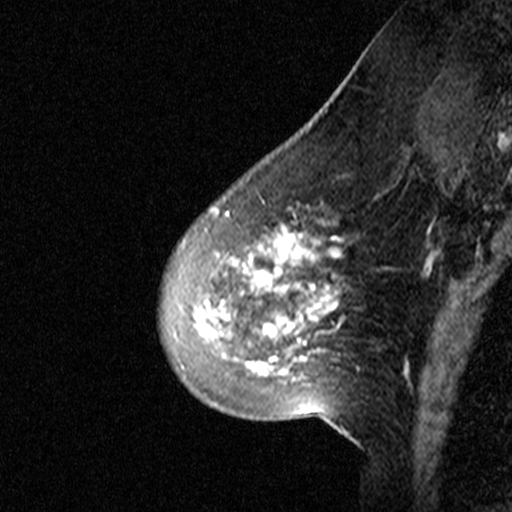
Breast MRI (dynamic contrast-enhanced), one sagittal slice. Slice 12 of 44 in the series (ordered by position). Dynamic contrast-enhanced study with each time point stored as its own series, time point 2 of 3 at this slice position (early post-contrast, ordered by acquisition time). 1.5 T. TE 4.5 ms, TR 11 ms. 3 mm slice thickness. 512 × 512 image matrix, field of view 200 × 200 mm. Patient: female, 46 years. Case-level facts recorded for this patient, not image findings: setting: breast cancer imaged before/during neoadjuvant chemotherapy; receptor status: HER2-positive.
Annotated regions visible in this slice (semi-automatically segmented with operator editing):
- analysis volume of interest (the breast-tissue region the enhancement analysis was run in; not a lesion): box from (x=157, y=172) to (x=359, y=393) px
- tumour enhancement mask (voxels above the 90 % enhancement threshold inside the analysis volume of interest): (x=196, y=213)–(x=341, y=374)